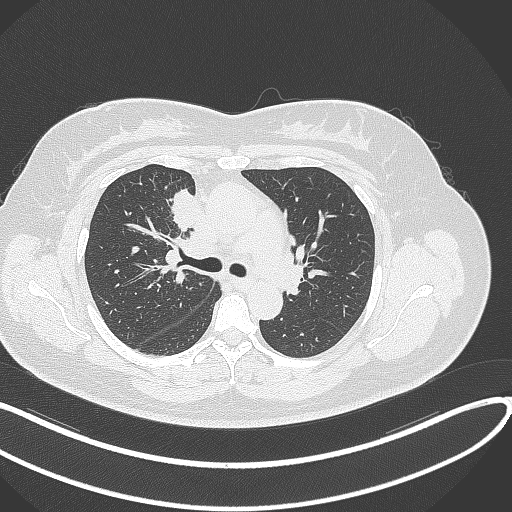
Chest CT, one axial slice. Slice 180 of 303 in the series (ordered by position). Reconstruction kernel B70f. 120 kVp. Lung window (W 1500 / L -600 HU). 1 mm slice thickness. 512 × 512 image matrix, field of view 400 × 400 mm. Patient: female, 46 years. Case-level facts recorded for this patient, not image findings: clinical TNM (as recorded): T2a N1 M0.
Annotated regions visible in this slice (rectangle marked by the reading radiologist):
- lung tumour (recorded histology: adenocarcinoma): bounding box <171,186,205,236> (left, top, right, bottom; pixels)